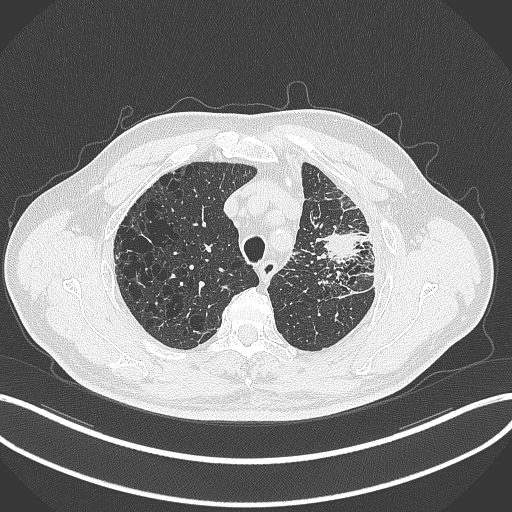
Chest CT, one axial slice. Position 257 of 297 along the scan axis. 120 kVp. Lung window (W 1500 / L -600 HU). 1 mm slice thickness. 512 × 512 image matrix. Patient: male, 68 years. From the clinical record (not read from this slice): clinical TNM (as recorded): T3 N3 M1.
Structures marked on this image (rectangle marked by the reading radiologist):
- lung tumour (recorded histology: adenocarcinoma): bounding box <317,221,365,265> (left, top, right, bottom; pixels)